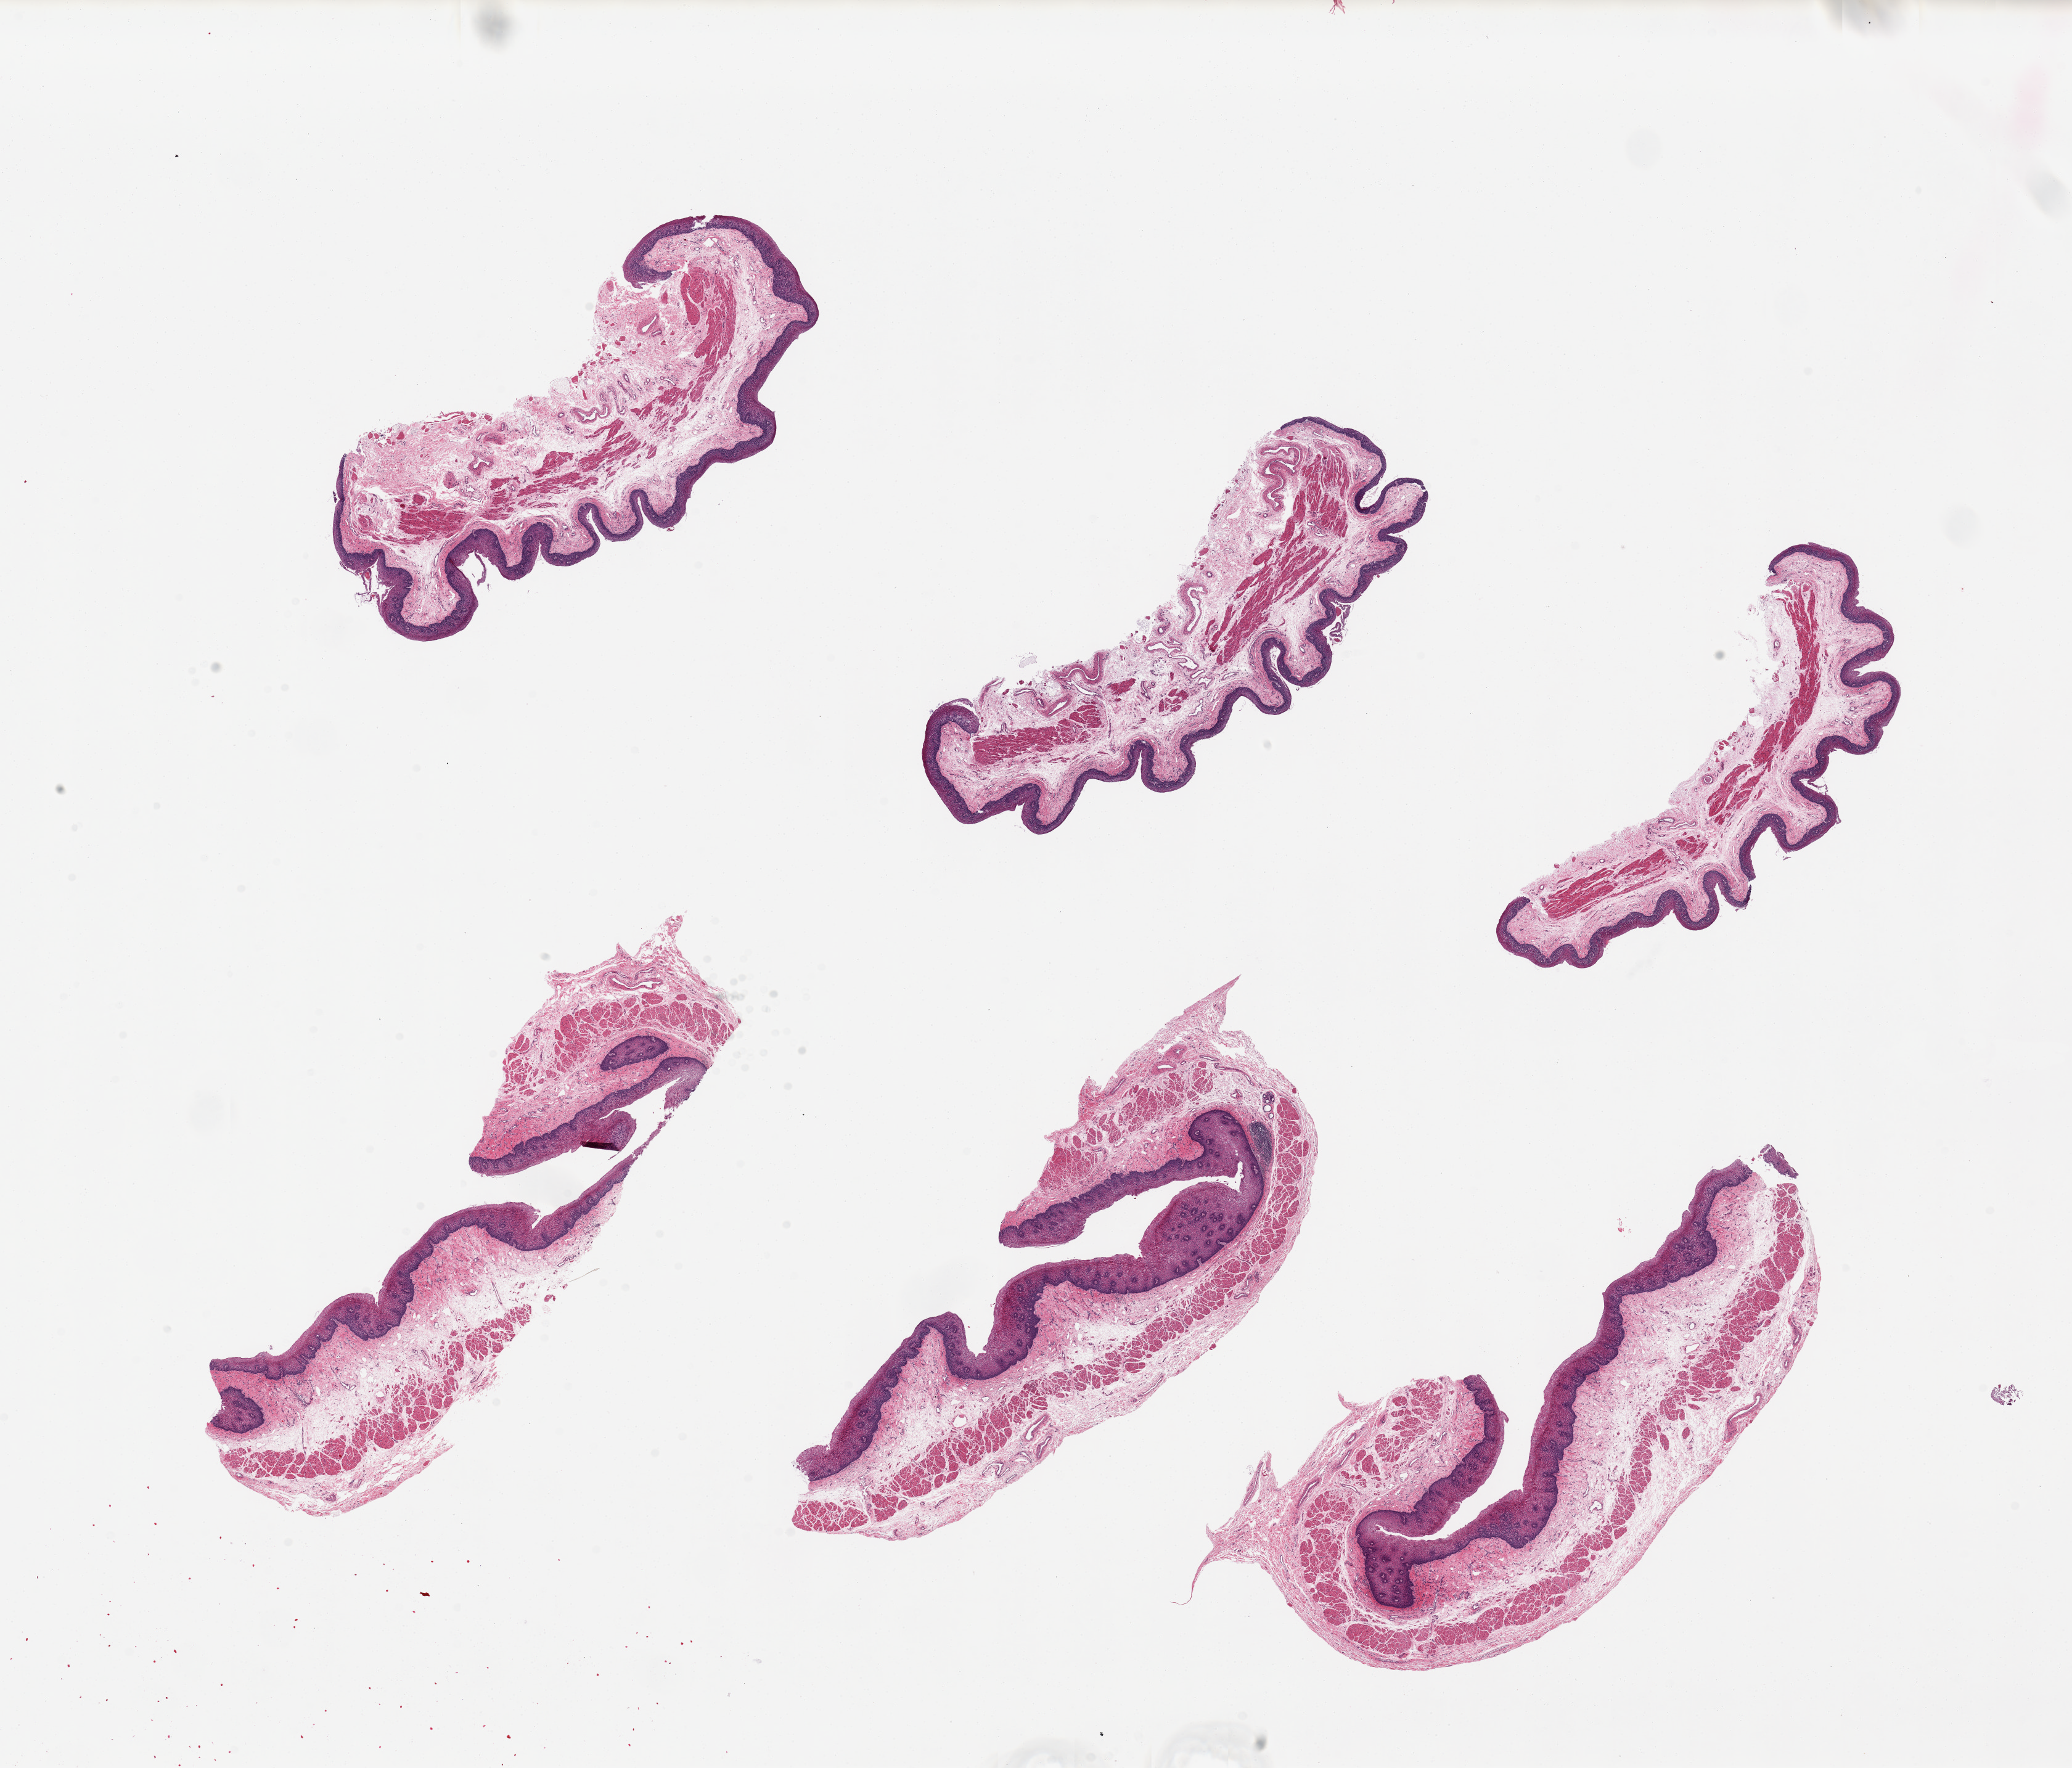
Digitized hematoxylin and eosin (H&E)-stained section — whole scanned area (about 26.6 x 22.7 mm, slide scanned at 20x) shown as a low-resolution overview, PAXgene-fixed, paraffin-embedded tissue, section of esophageal mucous membrane (target tissue), tissue donor sample. Donor sex: female.
Review note (as recorded): 6 pieces. up to 9.5x4mm; Well dissected.